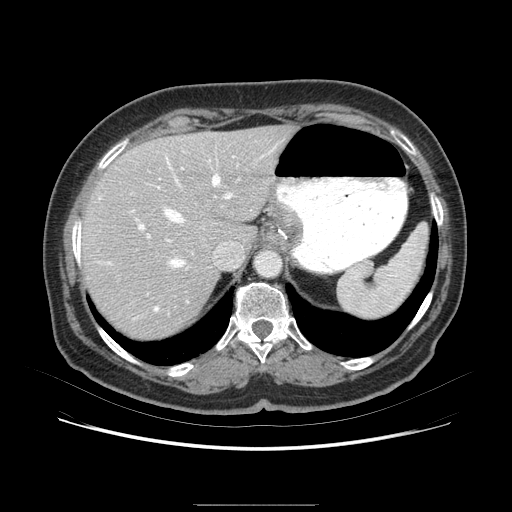
Contrast-enhanced abdominal CT (liver protocol), one axial slice. Position 58 of 79 along the scan axis. 120 kVp. Soft-tissue window (W 400 / L 40 HU). 512 × 512 image matrix, field of view 380 × 380 mm. From the clinical record (not read from this slice): diagnosis: hepatocellular carcinoma (patient treated with transarterial chemoembolisation; whether this scan precedes or follows treatment is not stated here); TNM stage (as recorded): Stage-I; Child-Pugh class: A; tumour nodularity: uninodular.
Structures marked on this image (semi-automatic segmentation, software-assisted and operator-edited):
- liver parenchyma outside the tumour (the mass and vessels are separate outlines, so this box may not span the whole liver): box from (x=82, y=130) to (x=301, y=324) px
- liver vessels: (x=123, y=157)–(x=247, y=251)